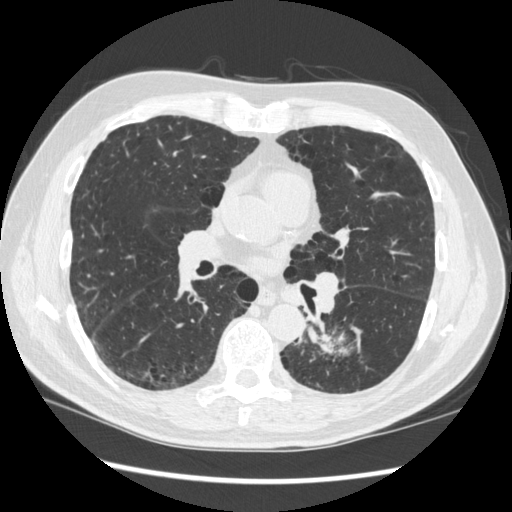
Low-dose screening chest CT, axial slice, baseline annual screen, lung window (W 1500 / L -600 HU), 1.25 mm slice thickness, standard (soft-tissue) reconstruction kernel (STANDARD), 120 kVp, slice 169 of 348 in the series, 512 × 512 image matrix. Male participant, aged 72 years at enrolment.
Lesion marked by an expert reader, box from (x=263, y=306) to (x=369, y=401) px. The screening reader recorded 2 non-calcified nodules or masses ≥4 mm on this exam; which of them this box marks is not recorded. Participant outcome: lung cancer diagnosed 37 days after this screen — squamous cell carcinoma, NOS, left lower lobe, stage IIIA (AJCC 6th edition), 60 mm at pathology.